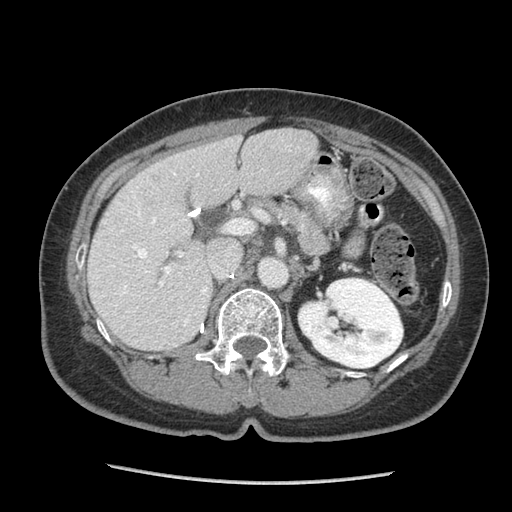
Contrast-enhanced abdominal CT (liver protocol), one axial slice. Slice 43 of 105 in the series (ordered by position). Reconstruction kernel STANDARD. Soft-tissue window (W 400 / L 40 HU). 2.5 mm slice thickness. 512 × 512 image matrix. Case-level facts recorded for this patient, not image findings: diagnosis: hepatocellular carcinoma (patient treated with transarterial chemoembolisation; whether this scan precedes or follows treatment is not stated here); TNM stage (as recorded): Stage-I; Child-Pugh class: A; tumour nodularity: uninodular.
Outlined on this slice (semi-automatically segmented with operator editing):
- liver parenchyma outside the tumour (the mass and vessels are separate outlines, so this box may not span the whole liver): bounding box (x1, y1, x2, y2) in pixels: (88, 128, 316, 350)
- liver vessels: (112, 150, 291, 325)